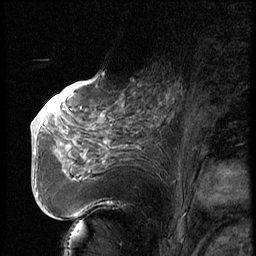
Breast MRI (dynamic contrast-enhanced), one sagittal slice. Slice 33 of 74 in the series (ordered by position). Dynamic contrast-enhanced series, image 2 of 3 at this slice position (ordered by acquisition). 1.5 T. TE 4.2 ms, TR 9 ms. 2.5 mm slice thickness. 256 × 256 image matrix, field of view 180 × 180 mm. Female patient, age 56 years. Case-level facts recorded for this patient, not image findings: setting: breast cancer imaged before/during neoadjuvant chemotherapy.
Structures marked on this image (semi-automatic segmentation, software-assisted and operator-edited):
- analysis volume of interest (the breast-tissue region the enhancement analysis was run in; not a lesion): bounding box (x1, y1, x2, y2) in pixels: (123, 71, 195, 131)
- tumour enhancement mask (voxels above the 140 % enhancement threshold inside the analysis volume of interest): (165, 85, 178, 117)